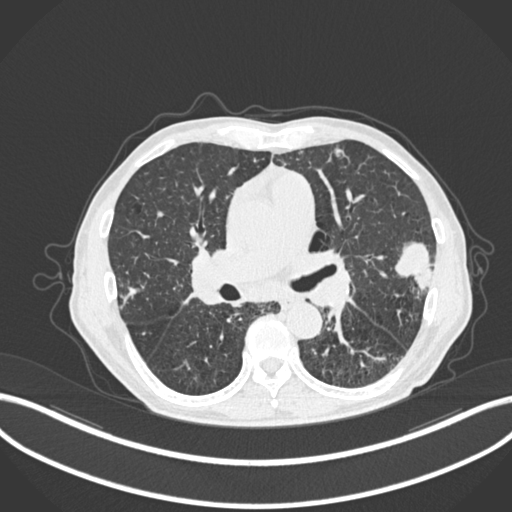
Chest CT, one axial slice. Slice 130 of 287 in the series (ordered by position). Reconstruction kernel B30f. Lung window (W 1500 / L -600 HU). 512 × 512 image matrix, field of view 400 × 400 mm. Male patient, age 74 years. Case-level facts recorded for this patient, not image findings: clinical TNM (as recorded): T2a N1 M0.
Outlined on this slice (bounding box drawn by a radiologist):
- lung tumour (recorded histology: adenocarcinoma): bounding box [x1, y1, x2, y2] px = [396, 236, 432, 290]